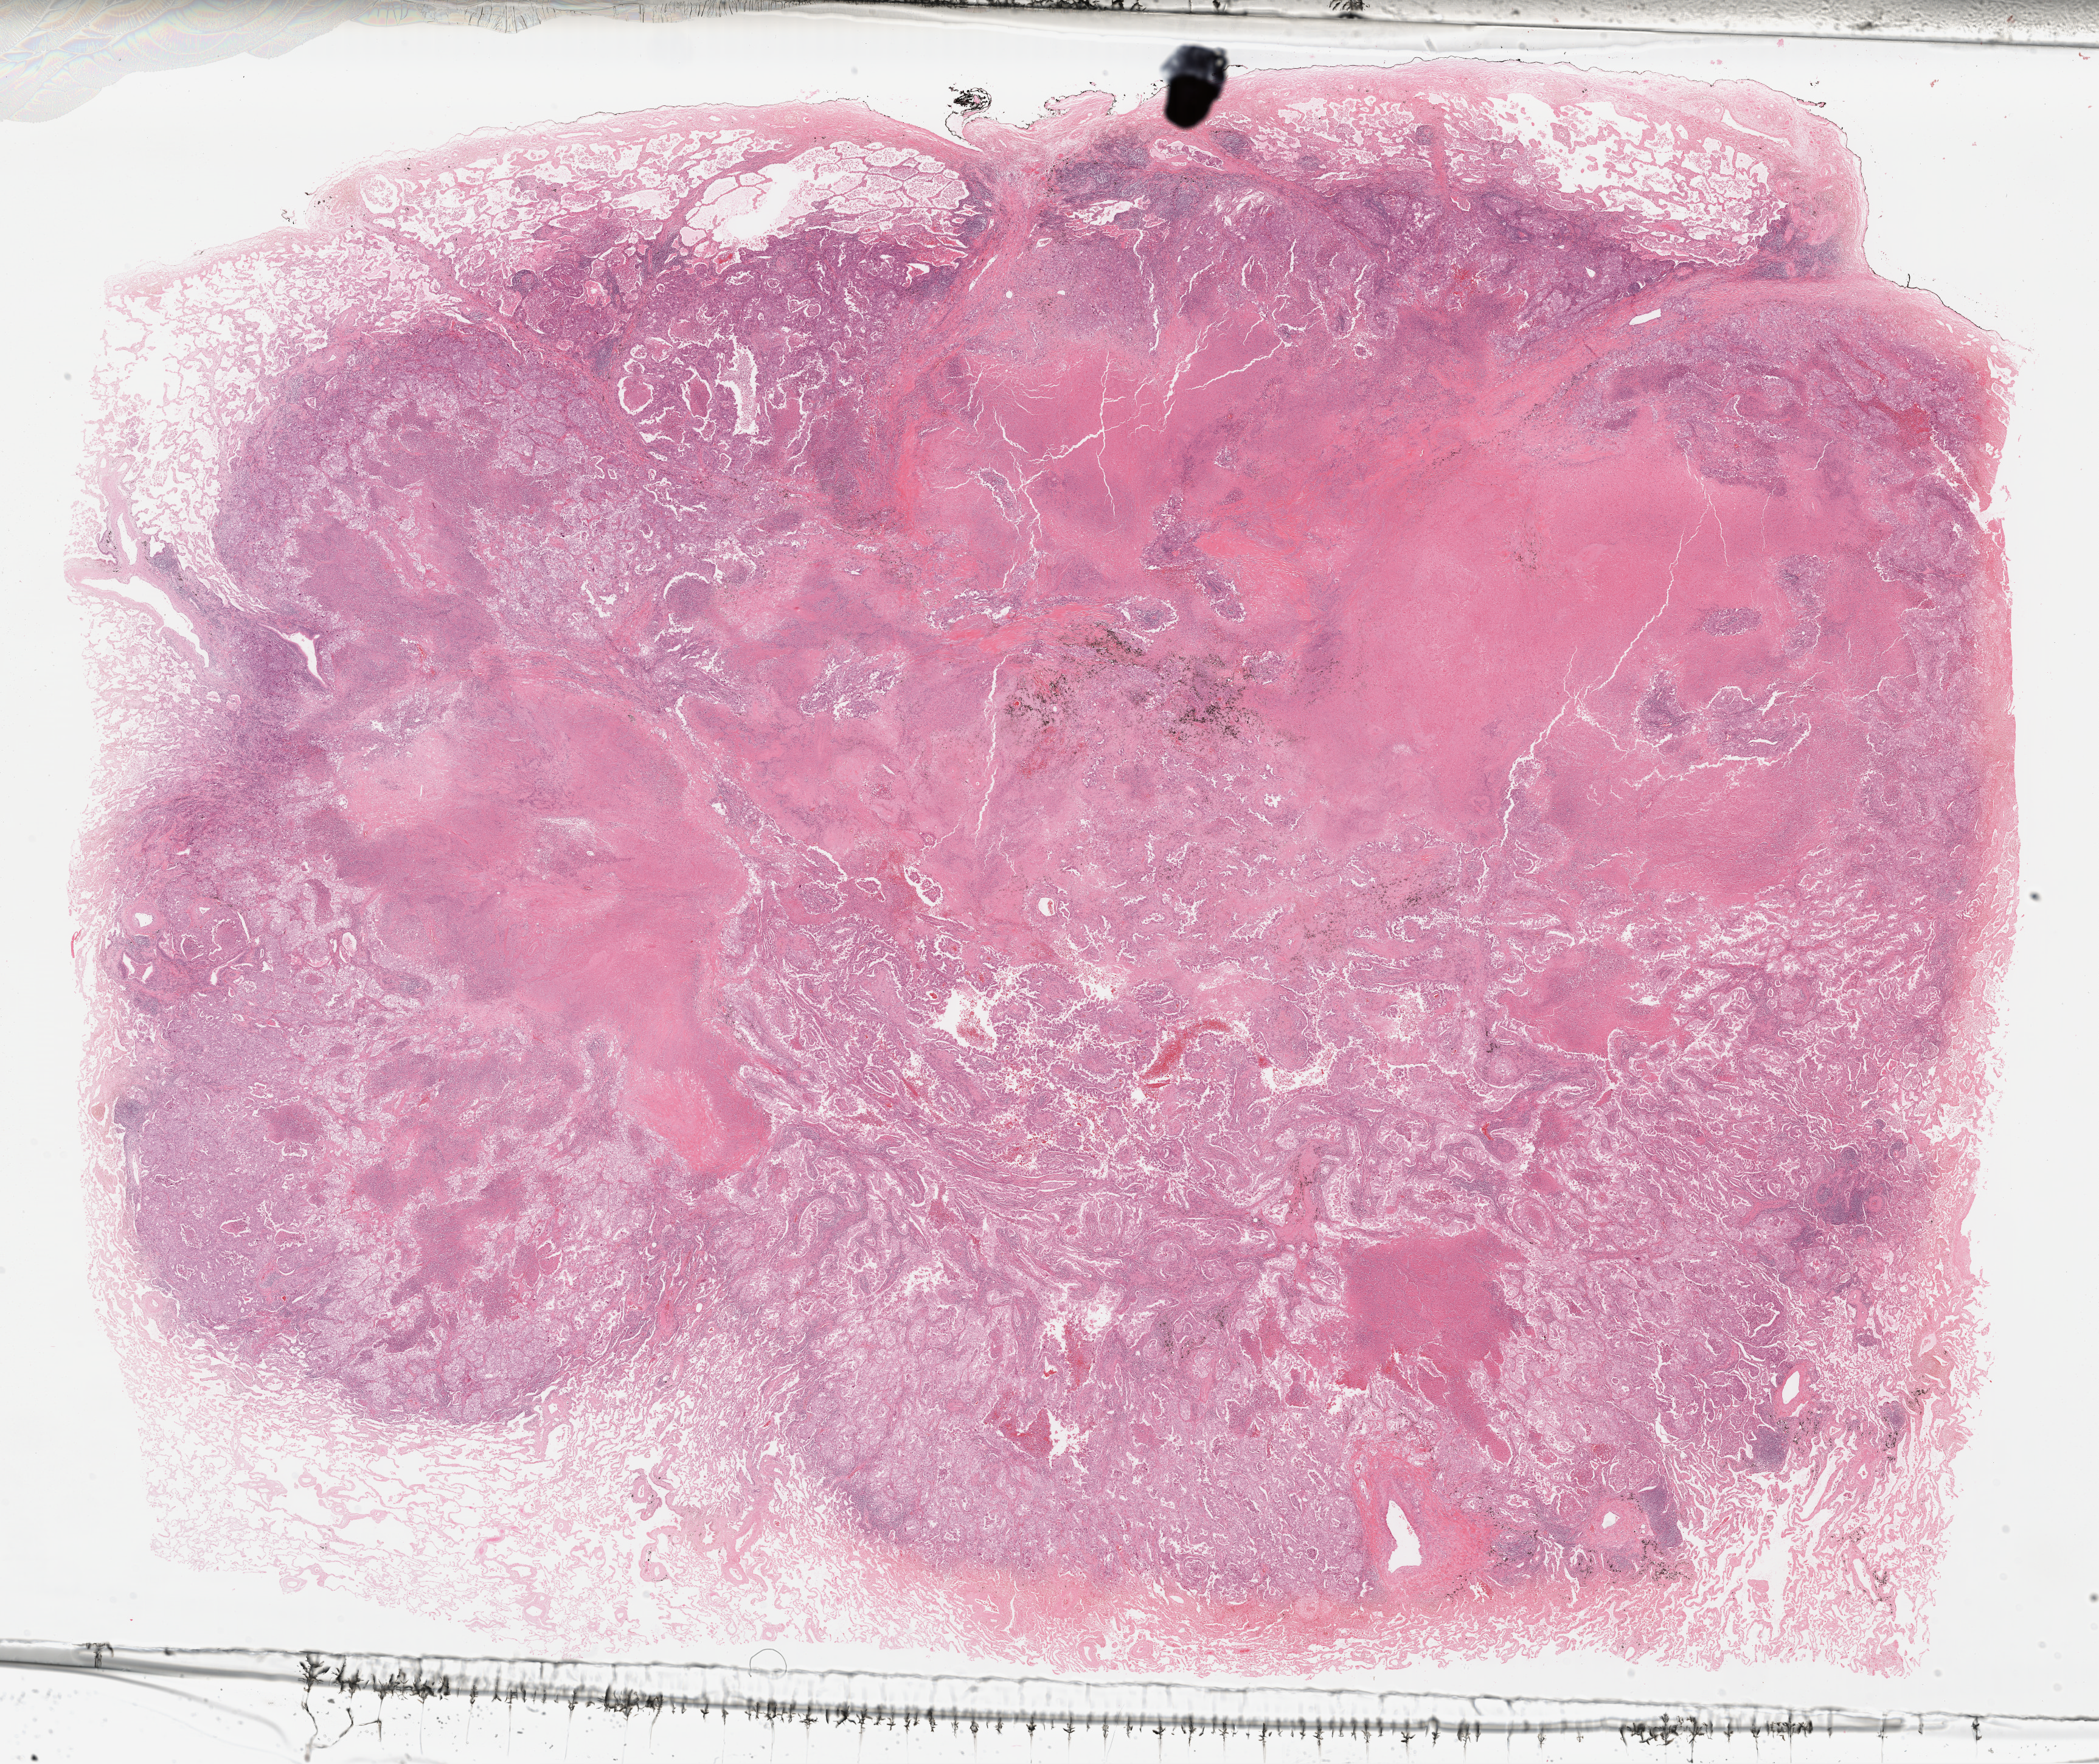
Digitized Hematoxylin and eosin (H&E) stained tissue section (whole slide), low-resolution overview of the scanned area, about 27.1 x 22.8 mm (slide scanned at 40x). FFPE section. Sample: primary tumour, lung. Patient: male, age at initial diagnosis 69 years.
Pathologic diagnosis: Adenocarcinoma, NOS (lower lobe, lung). Laterality: right. AJCC pathologic stage: IIB.